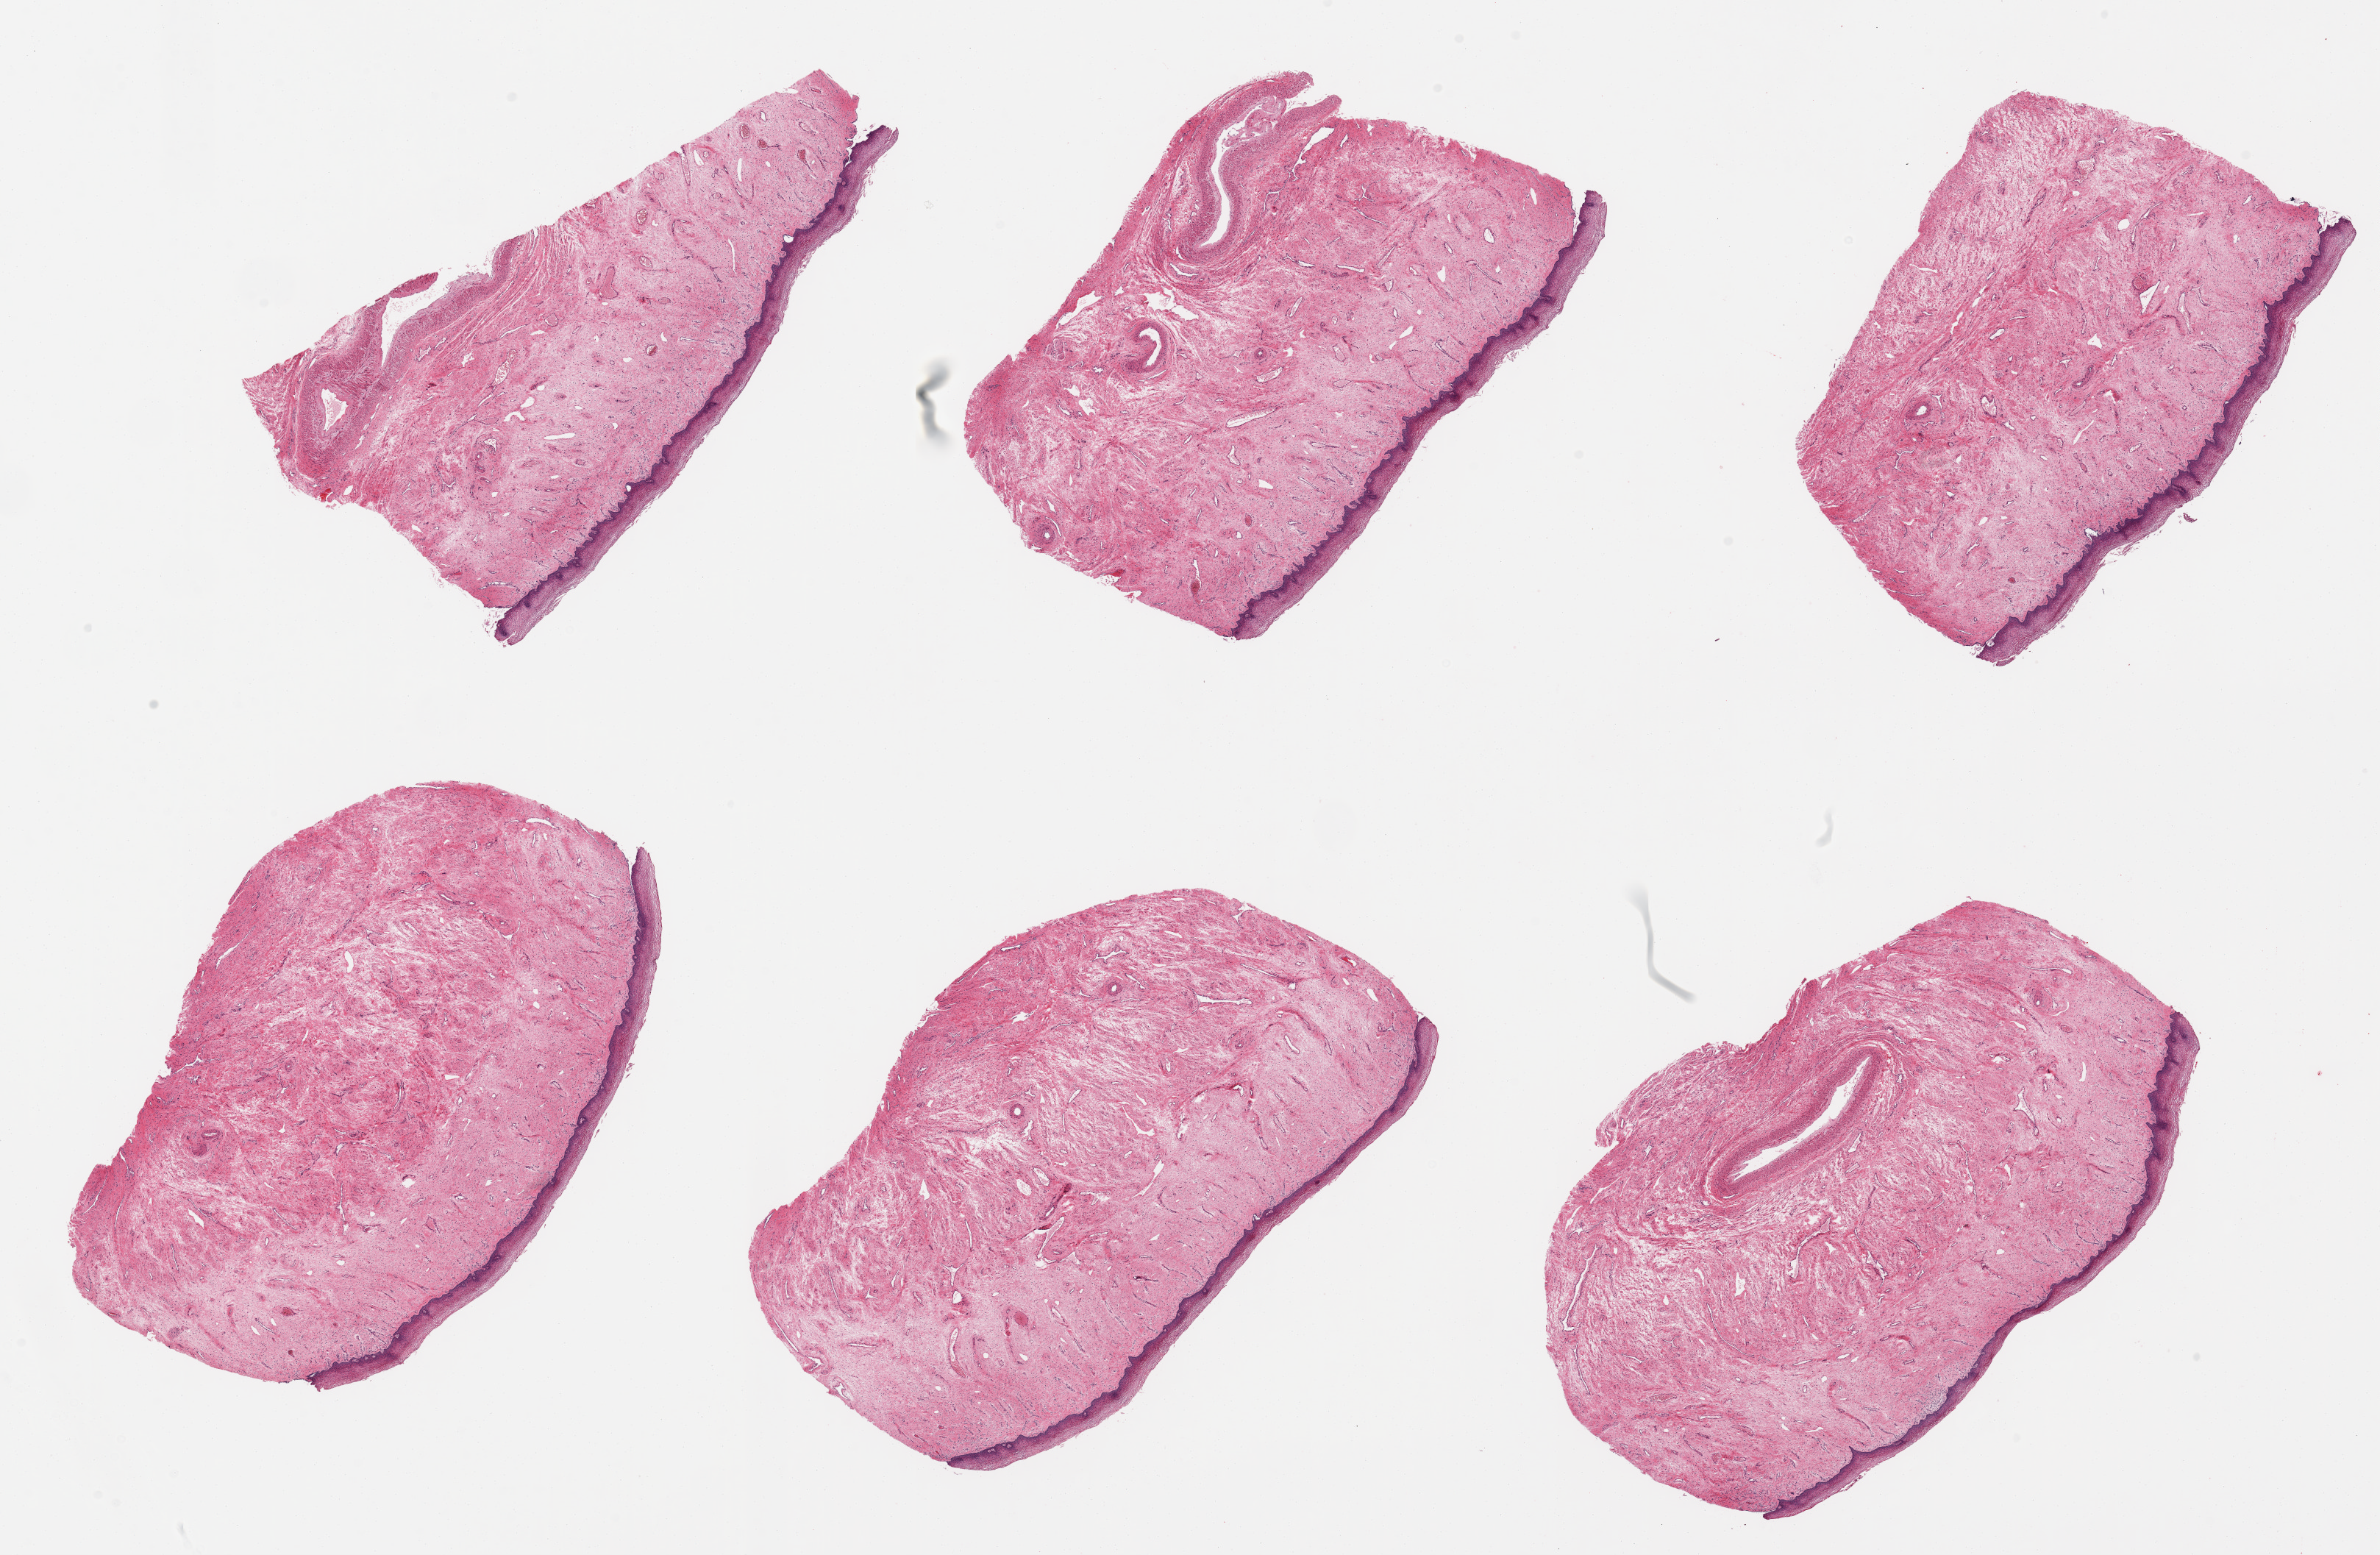
Digitized hematoxylin and eosin (H&E)-stained section — whole scanned area (about 25.6 x 16.7 mm) shown as a low-resolution overview, PAXgene-fixed, paraffin-embedded tissue, target tissue: vagina, tissue donor sample. Donor sex: female.
* review note (as recorded): 6 pieces, squamous epithelium is ~0.25mm